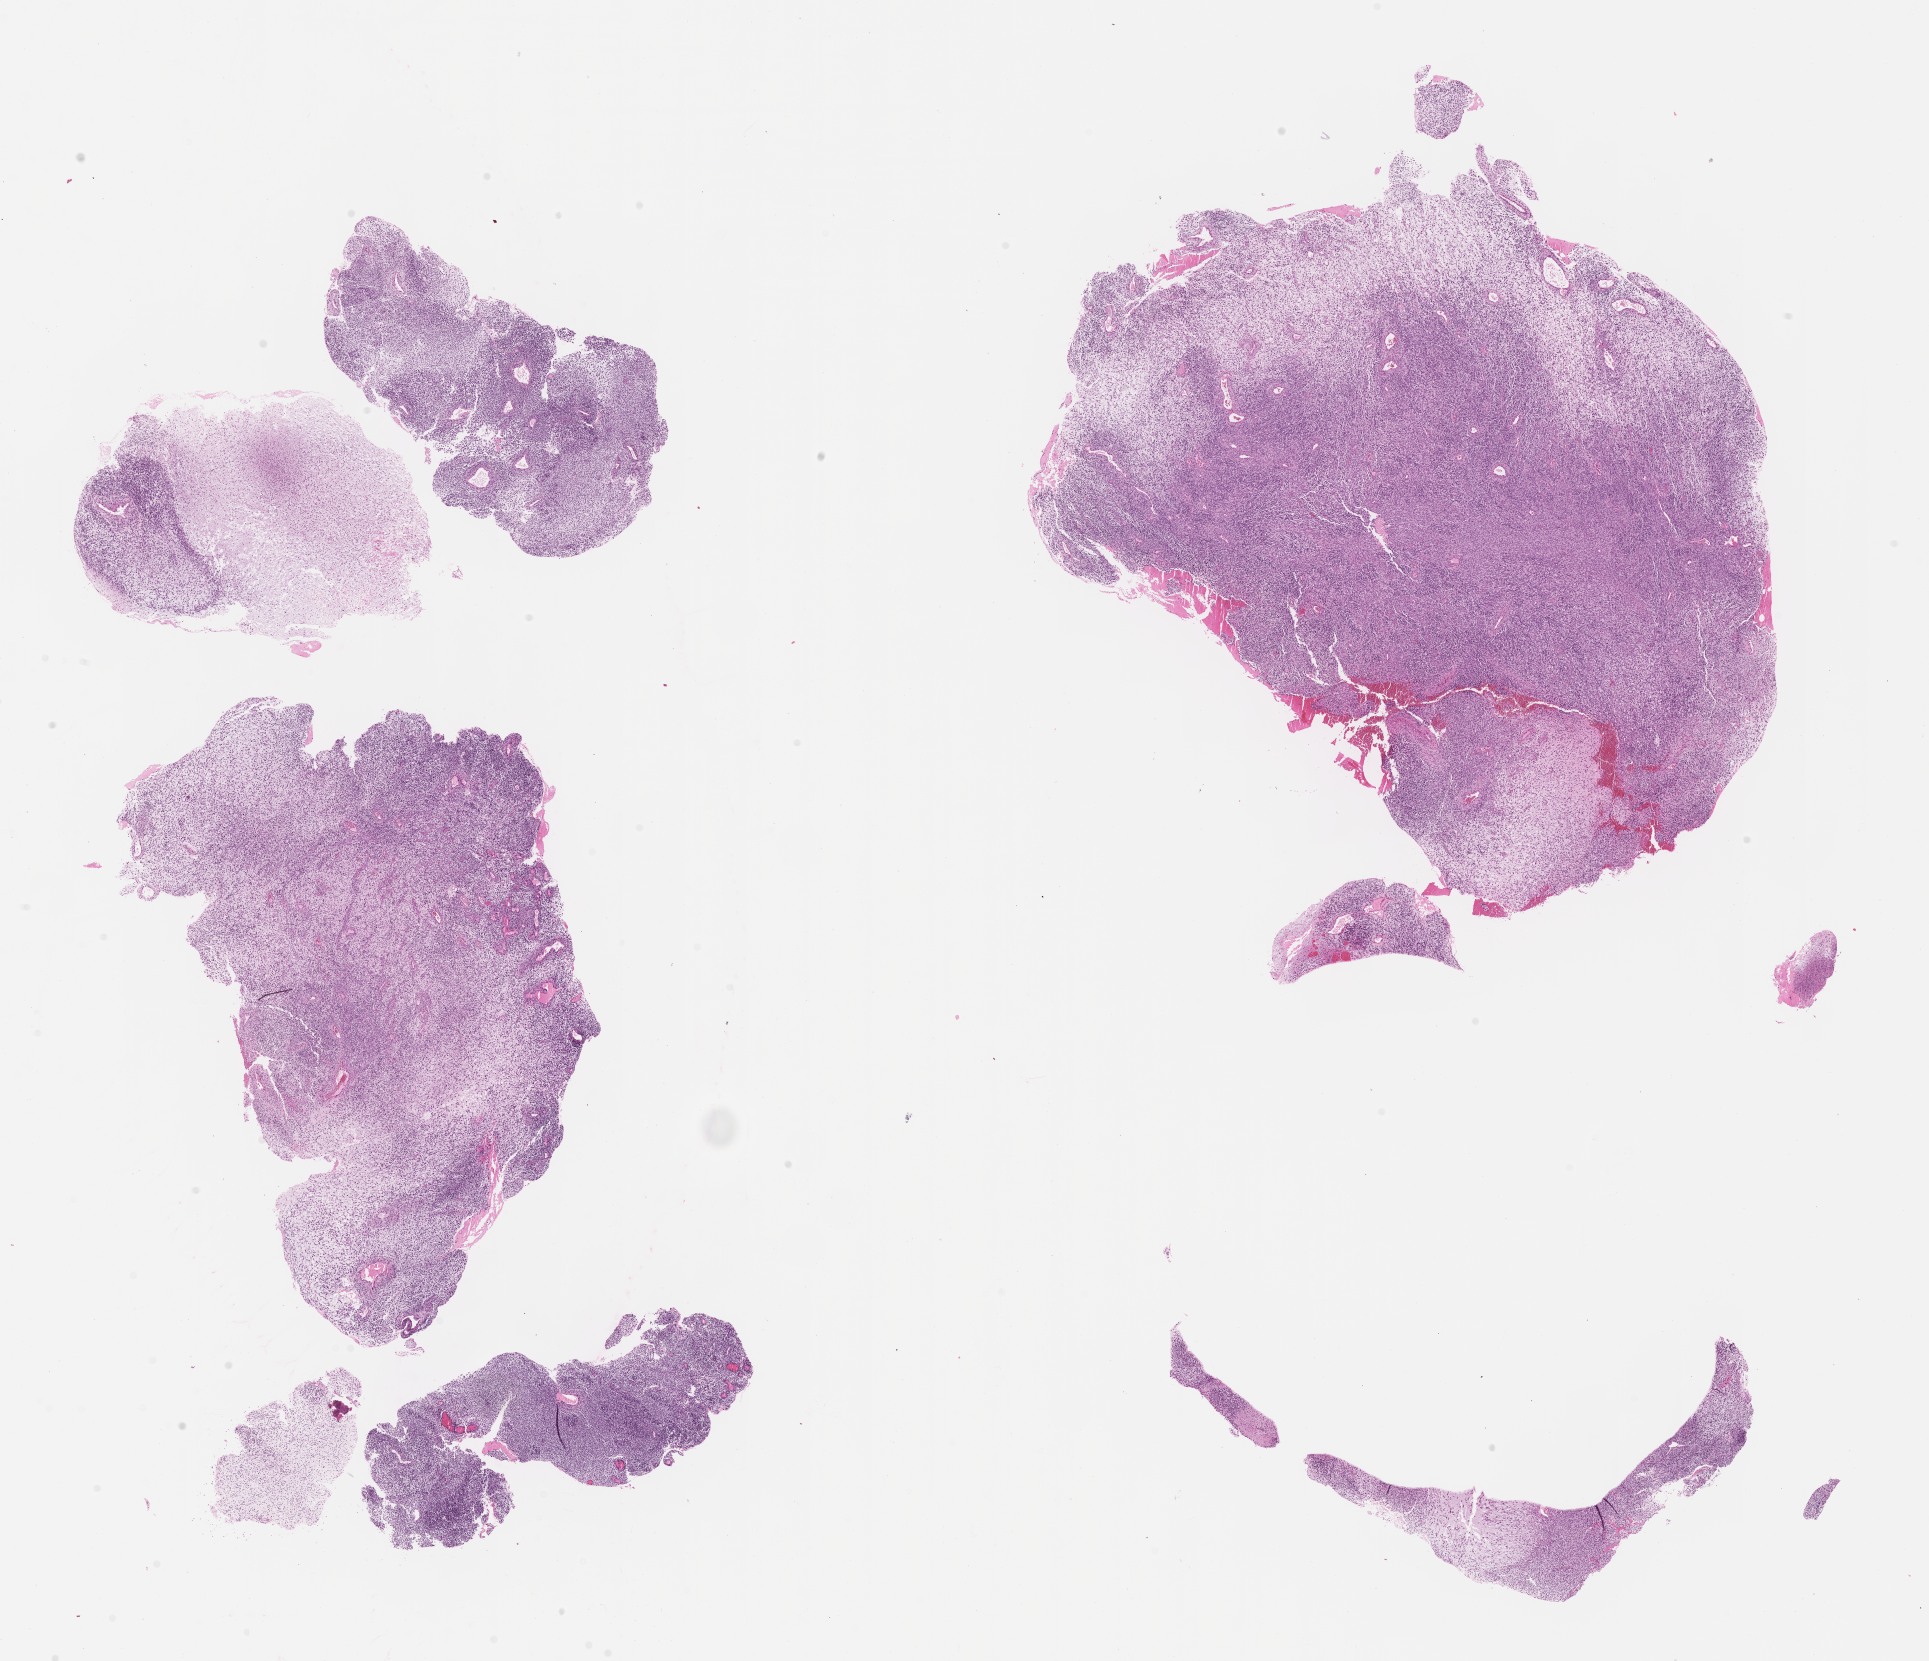
Hematoxylin and eosin (H&E) whole-slide image of tumor tissue, whole scanned area (about 15.6 x 13.4 mm) shown as a low-resolution overview; FFPE section; sample anatomic site: cheek, right. Patient: female, age 17.2 years at diagnosis.
• diagnosis: rhabdomyosarcoma; histological classification: embryonal rhabdomyosarcoma
• stage (as recorded): 1
• metastatic status at presentation (as recorded): non-metastatic (confirmed)